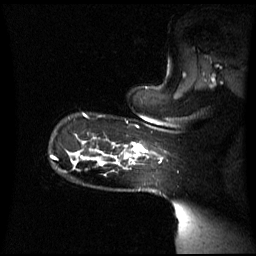
Breast MRI (dynamic contrast-enhanced), one sagittal slice; position 49 of 60 along the scan axis; dynamic contrast-enhanced series, image 2 of 3 at this slice position (ordered by acquisition); 1.5 T; TE 4.2 ms, TR 8.4 ms; 256 × 256 image matrix, field of view 270 × 270 mm. Patient: female, 39 years. Case-level facts recorded for this patient, not image findings: setting: breast cancer imaged before/during neoadjuvant chemotherapy; receptor status: triple-negative.
Structures marked on this image (semi-automatic segmentation, software-assisted and operator-edited):
- analysis volume of interest (the breast-tissue region the enhancement analysis was run in; not a lesion): bounding box [x1, y1, x2, y2] px = [101, 129, 161, 171]
- tumour enhancement mask (voxels above the 70 % enhancement threshold inside the analysis volume of interest): [126, 144, 147, 158]